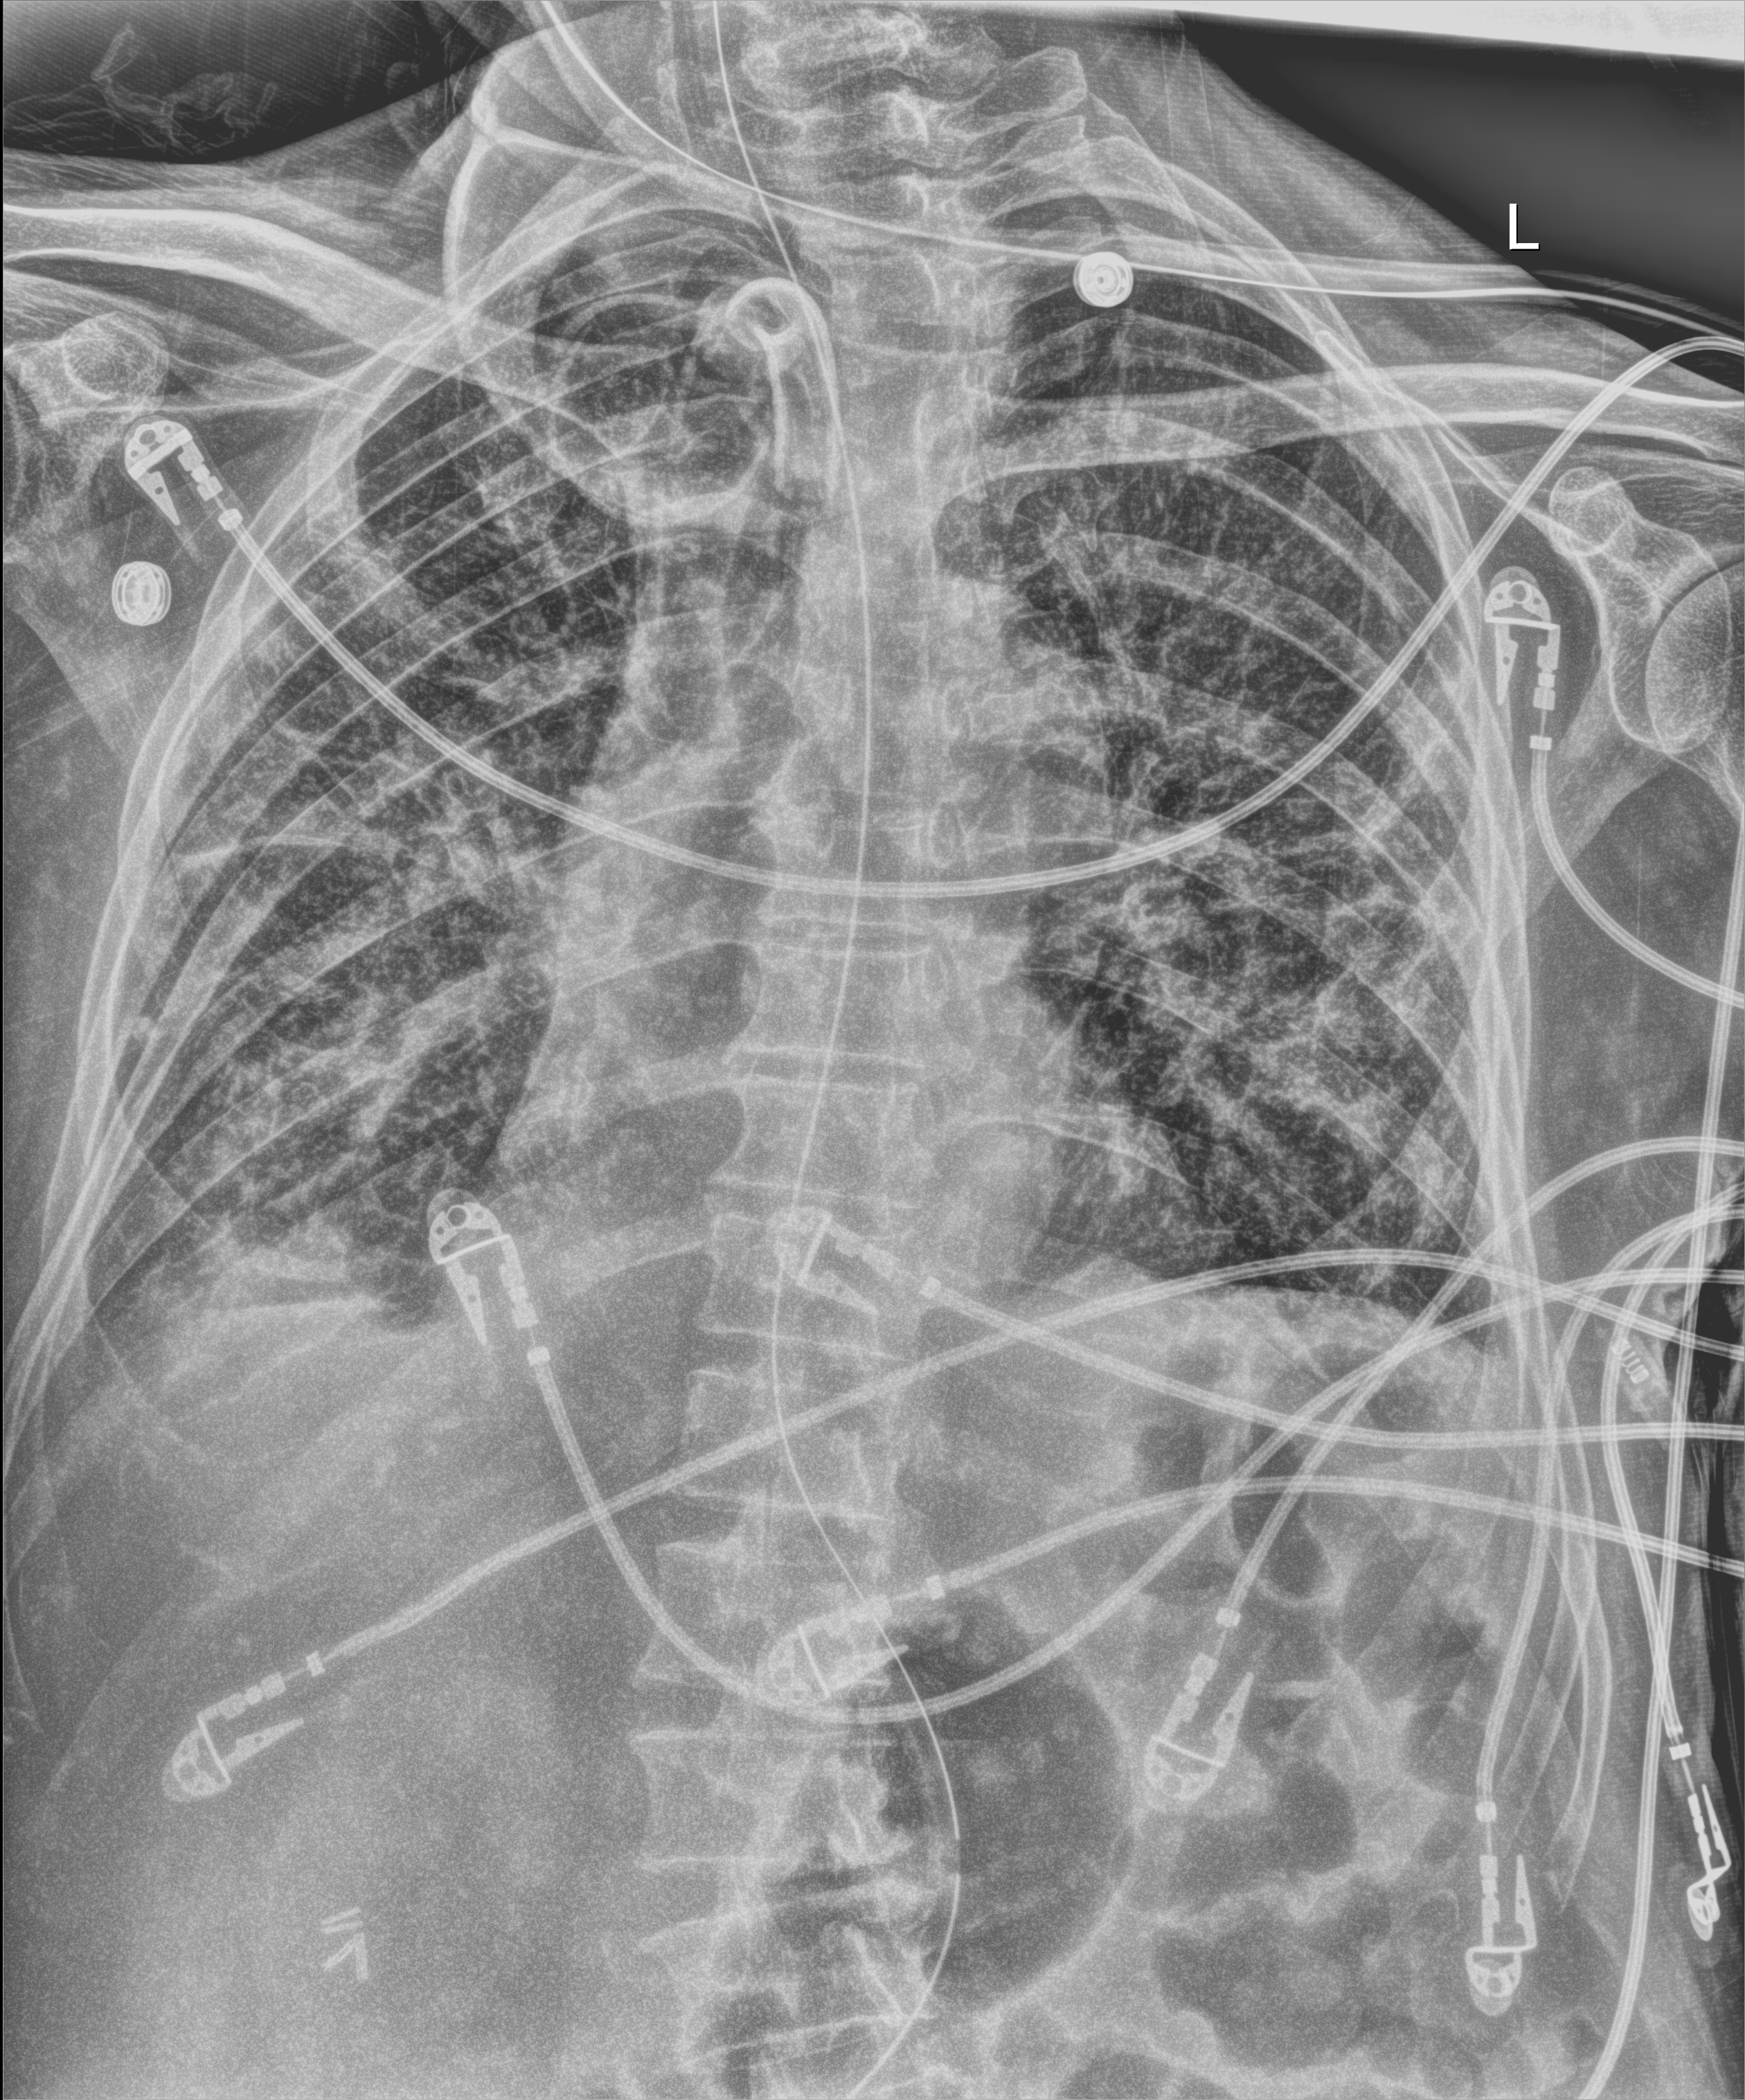
Portable chest radiograph, anteroposterior (AP) projection. Male patient hospitalised with COVID-19, age 75–90 years.
Hospital-stay facts (about this admission, not read from this image; timing relative to this image not recorded): admitted to intensive care during this hospital stay: yes; mechanically ventilated during this hospital stay: yes; smoking status (admission record): never.